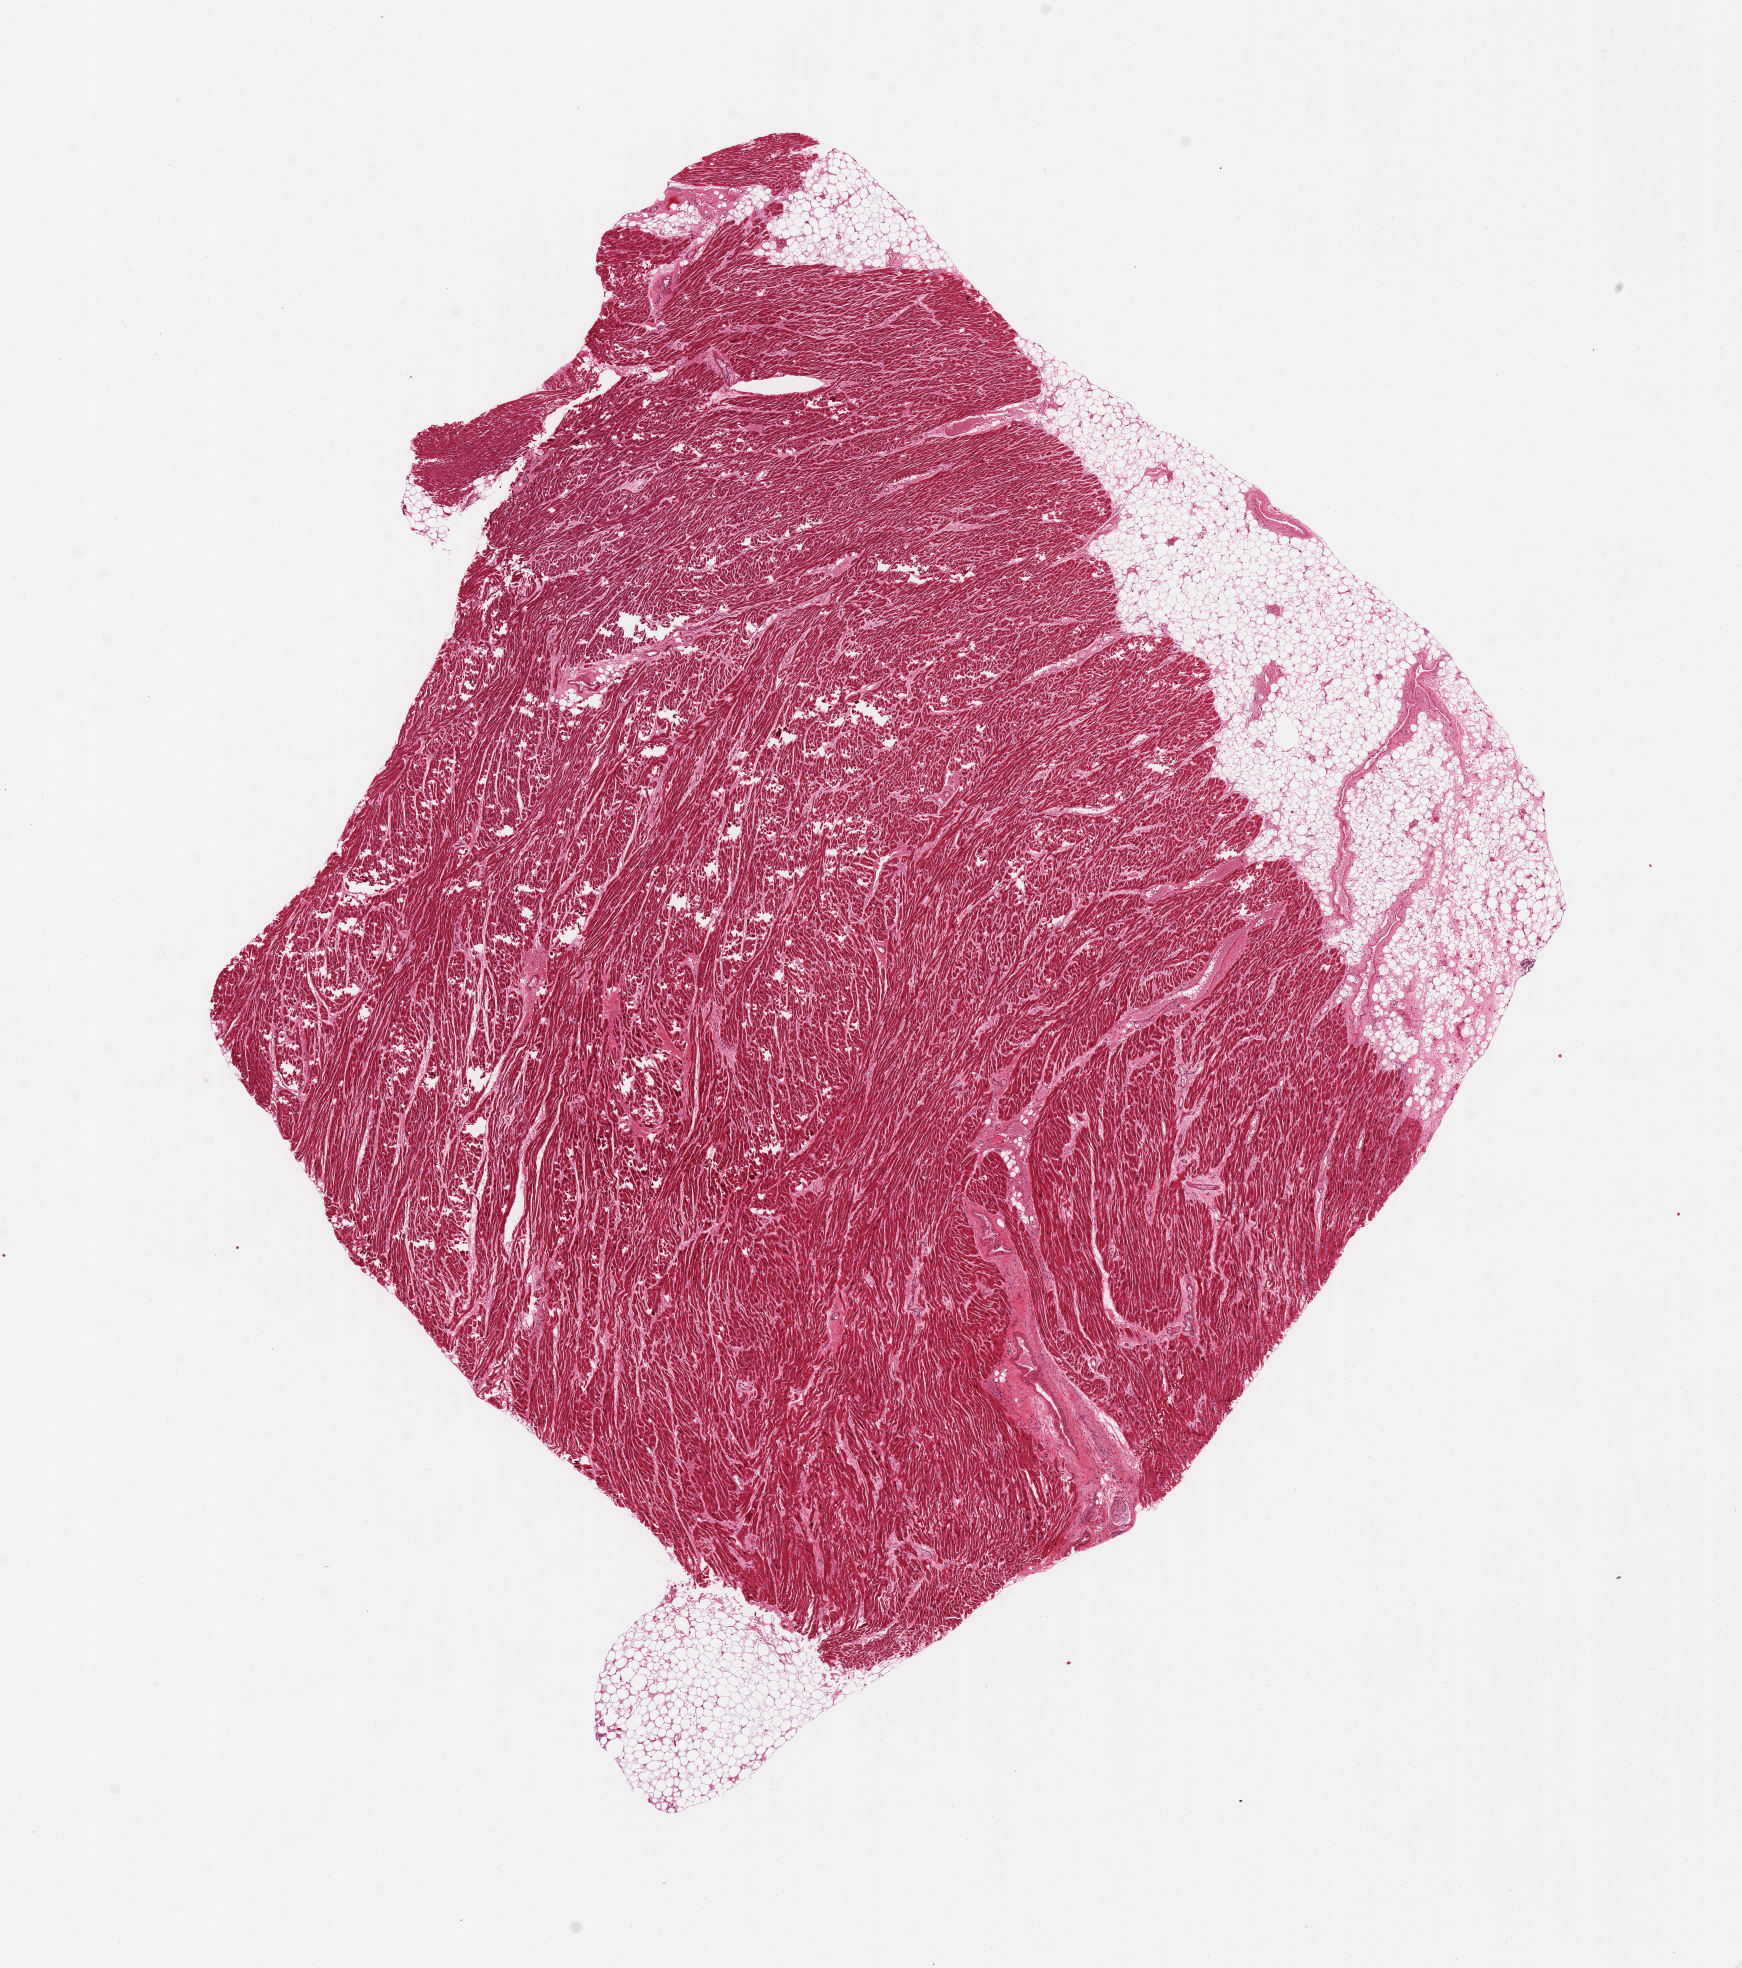
Whole-slide image, hematoxylin and eosin (H&E) stain, brightfield, shown as a low-resolution overview of the whole scanned area (about 13.8 x 15.6 mm), PAXgene-fixed paraffin-embedded (PFPE) section, sampled site (target tissue): heart, tissue donor sample. Donor: male.
Review note (as recorded): Early ischemia. Fat is 20% of aliquot. 9x9mm. Fracture artifacts.